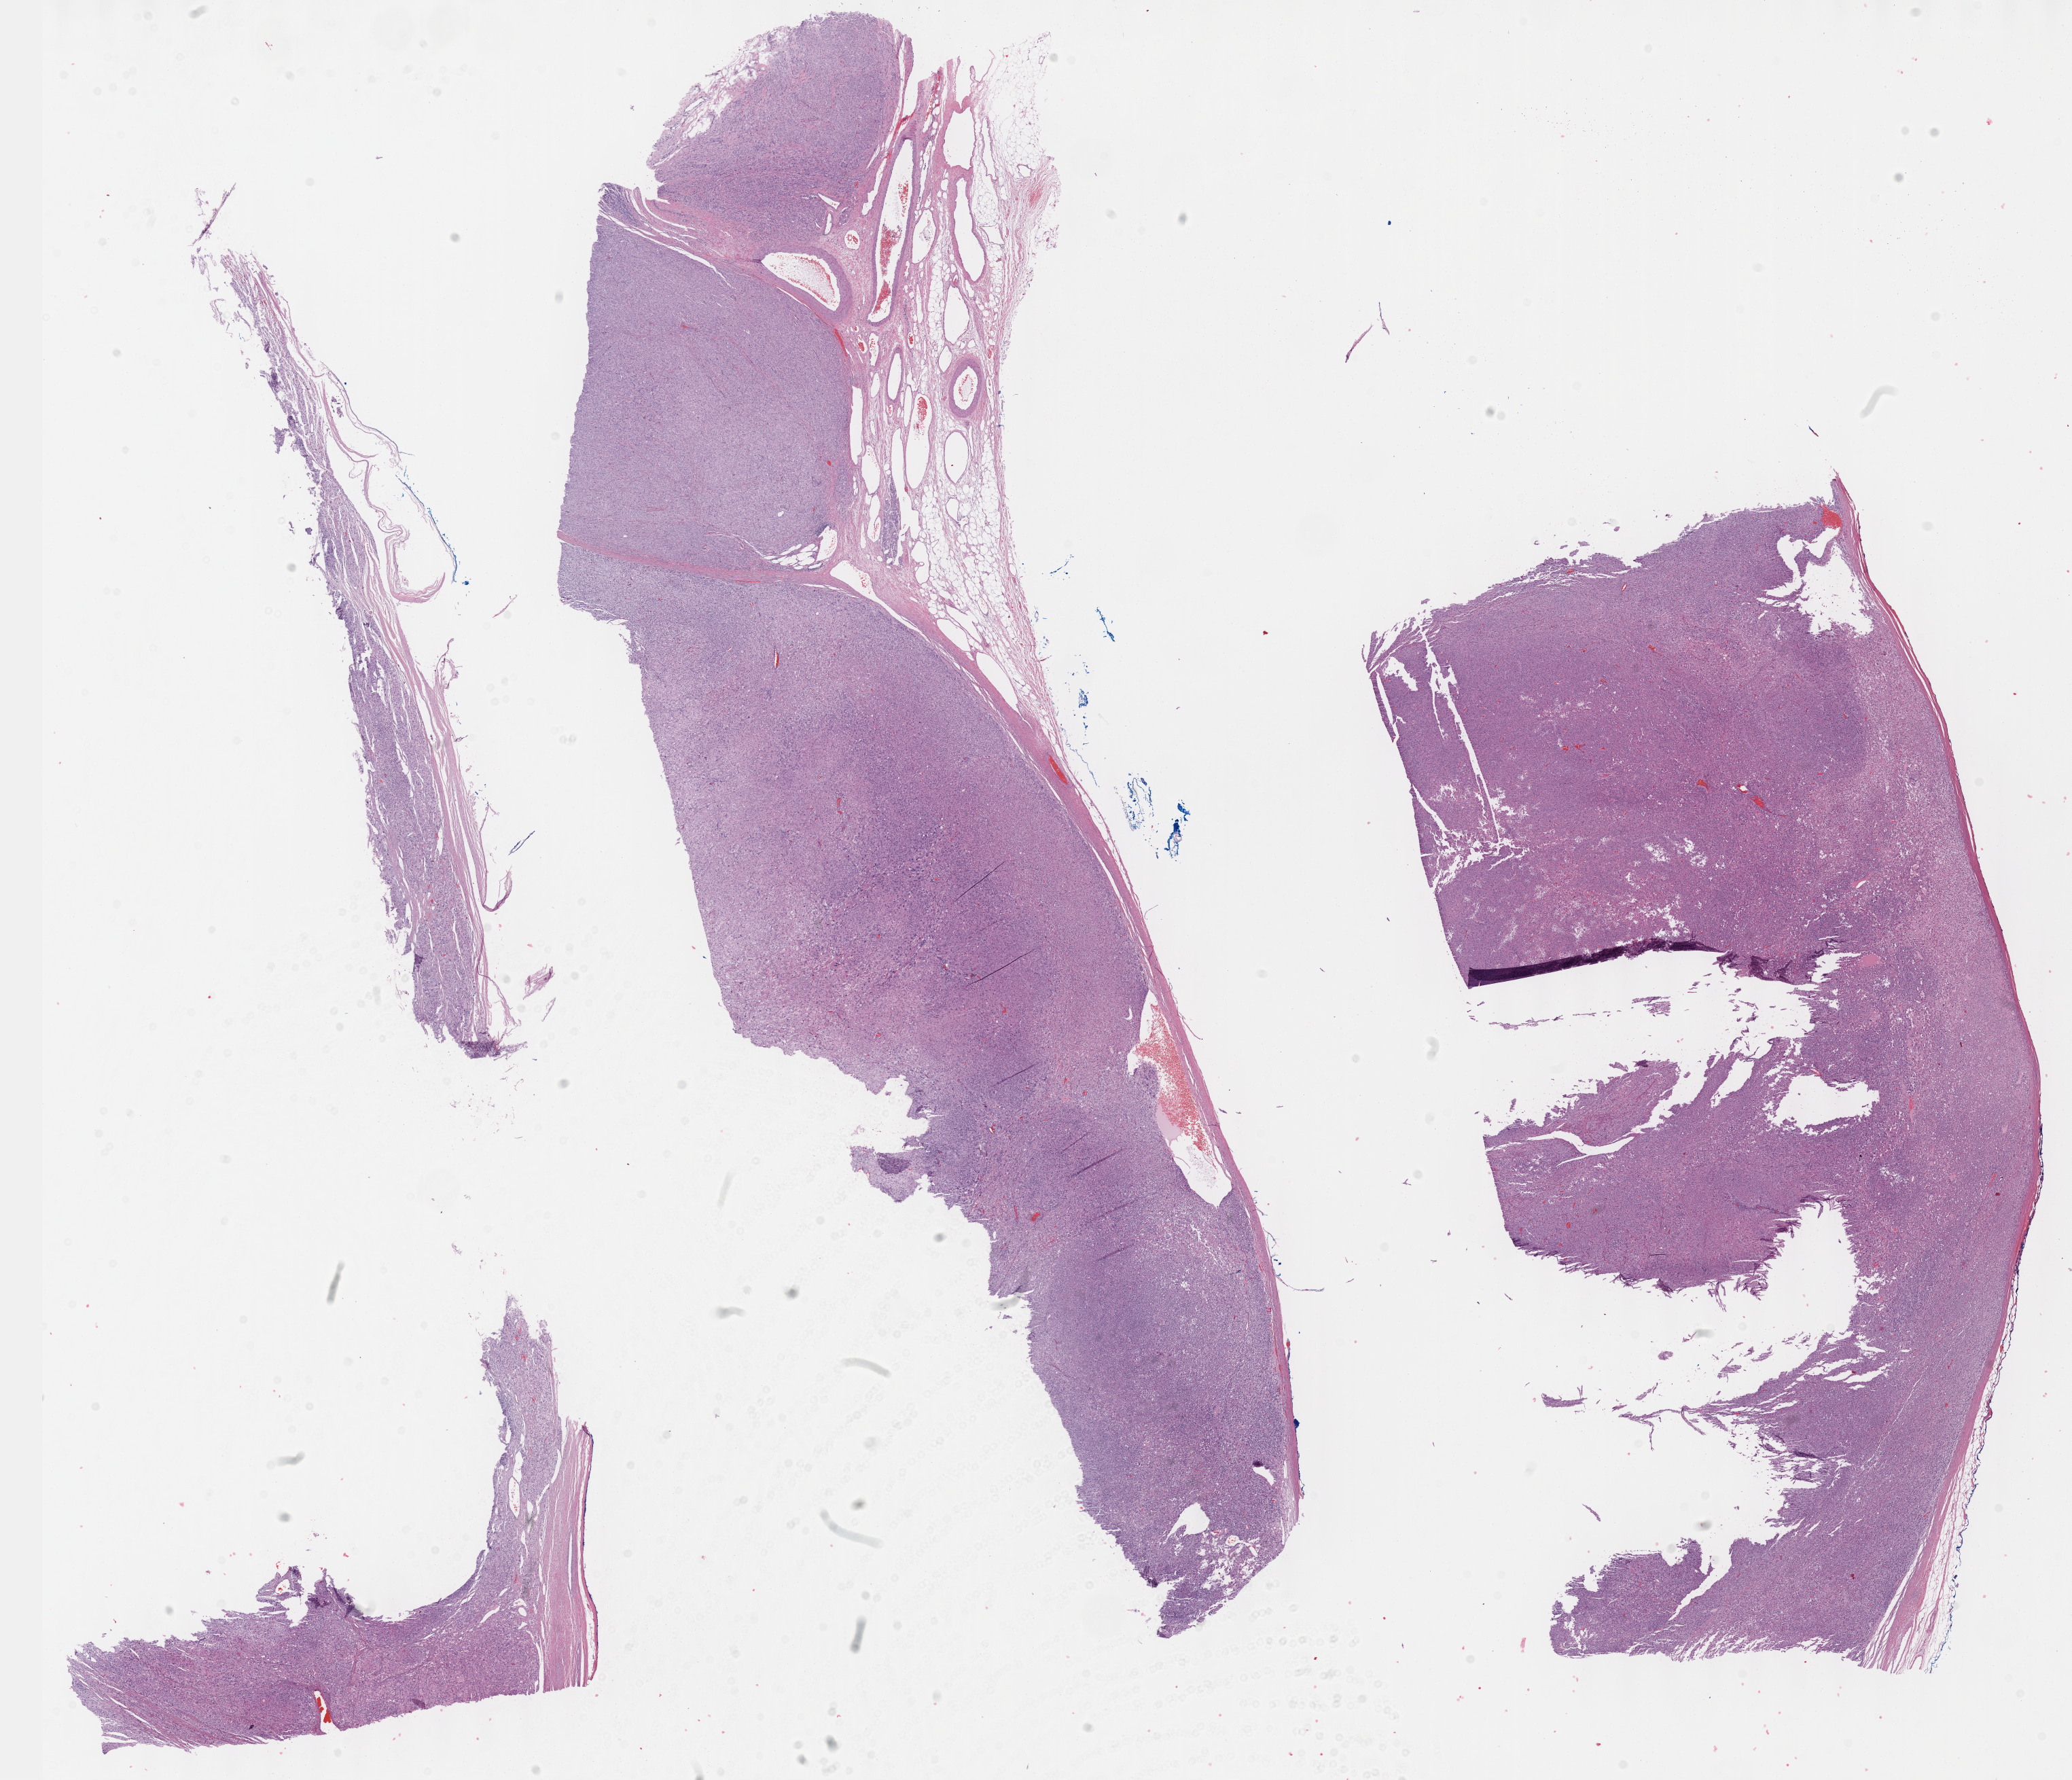
Whole-slide histology image, Hematoxylin and eosin (H&E) stained, shown as a low-resolution overview of the whole scanned area (about 24.6 x 21.2 mm, acquisition: 40x scan), formalin-fixed paraffin-embedded (FFPE) diagnostic section, primary tumour sample from the adrenal cortex. Patient: female, age at initial diagnosis 53 years.
Histologic diagnosis: Adrenal cortical carcinoma (cortex of adrenal gland).